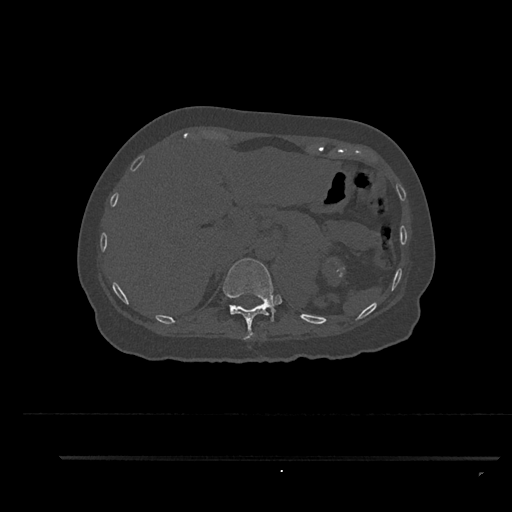
CT including the spine, one axial slice. Position 312 of 797 along the scan axis. Reconstruction kernel Br40s/3. Bone window (W 1800 / L 400 HU). 512 × 512 image matrix. Patient: female, 44 years. From the clinical record (not read from this slice): primary cancer: renal; vertebrae with lytic lesions (as recorded): L1.
Outlined on this slice (semi-automatic segmentation, software-assisted and operator-edited):
- T11 vertebra: bounding box <223,258,276,340> (left, top, right, bottom; pixels)